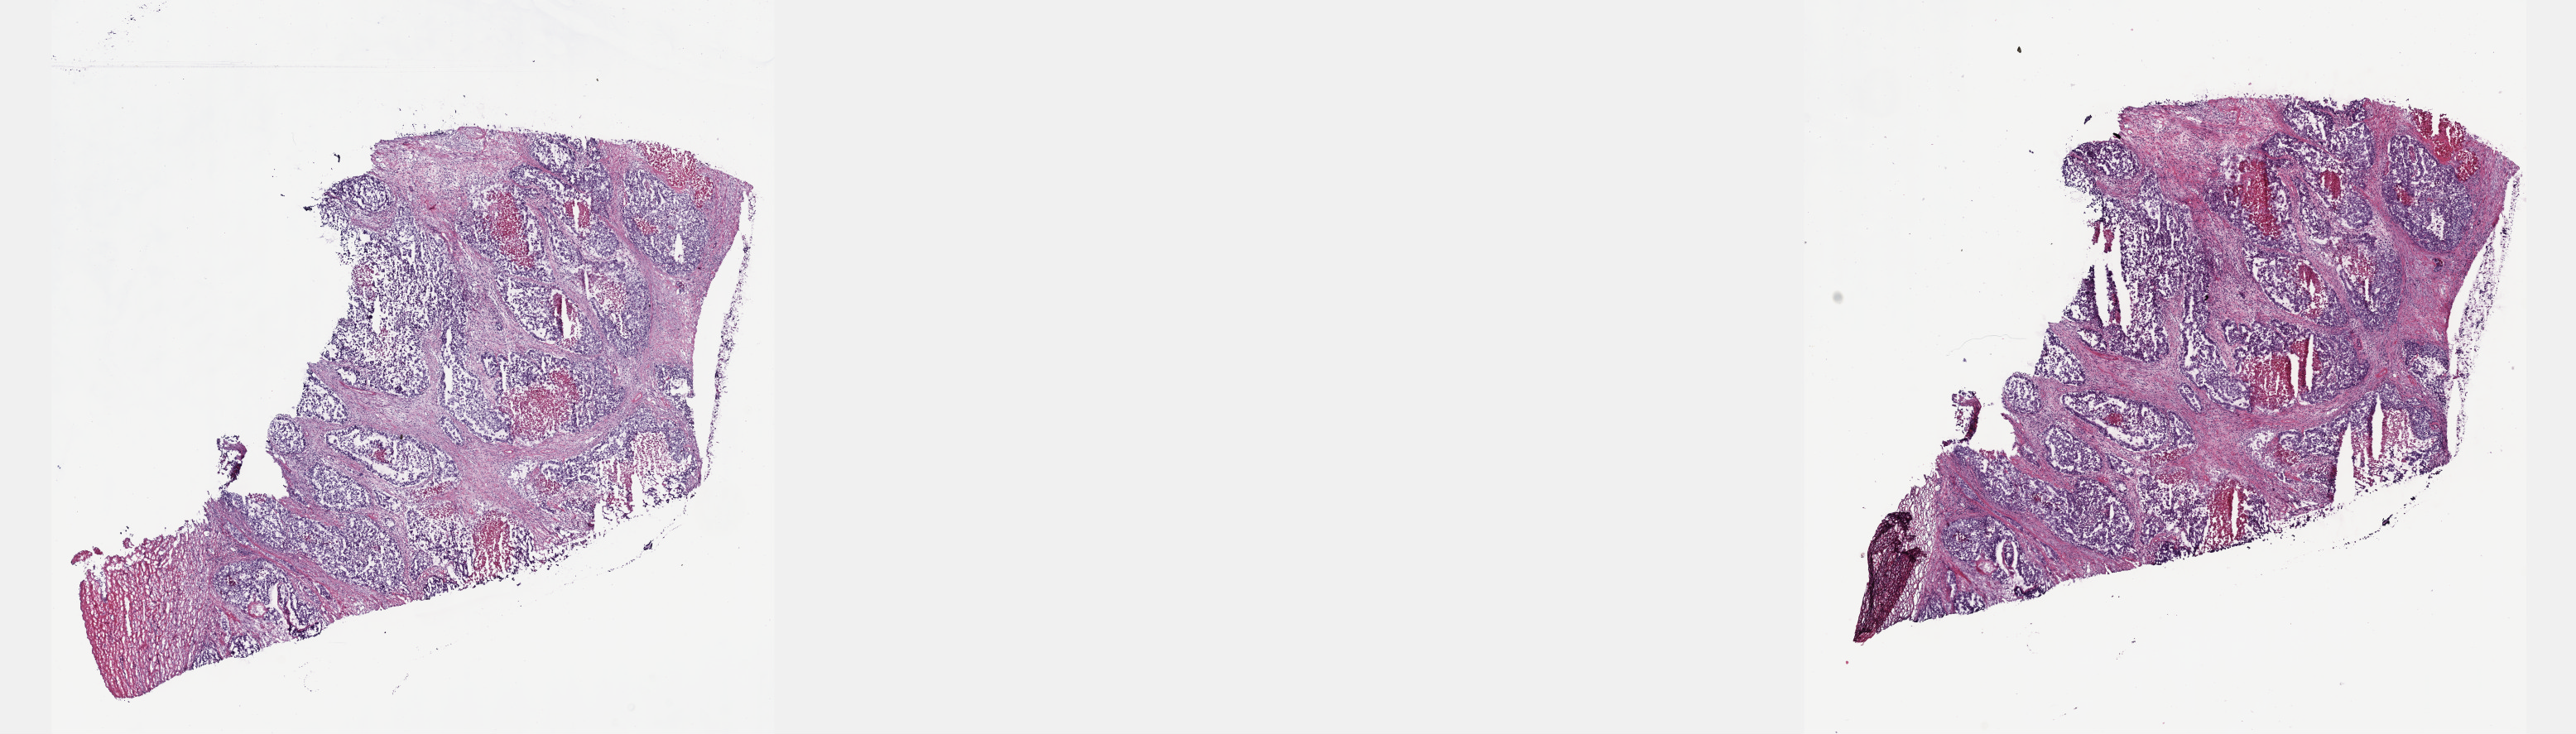
Hematoxylin and eosin (H&E) stained whole-slide image — shown as a low-resolution overview of the whole scanned area (about 25.1 x 7.2 mm, from a 40x scan). Frozen section from the top of the tissue portion. Sample: primary tumour, testis. Male patient; age at initial diagnosis 18 years. Pathologist review of this section (percent, as recorded): tumour cells 60%, tumour nuclei 60%, normal cells 0%, stromal cells 30%, necrosis 10%. Infiltration values recorded for this section: lymphocyte infiltration 40%, monocyte infiltration 20%, neutrophil infiltration 20%.
AJCC pathologic stage: III. Pathologic diagnosis: Embryonal carcinoma, NOS. Laterality: right.